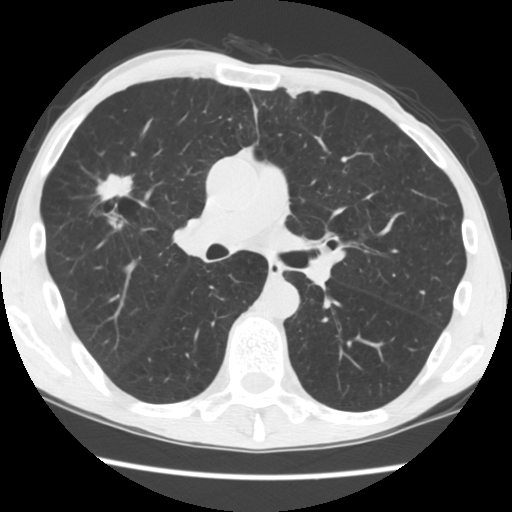
Axial slice from a low-dose chest CT screening exam; second annual screen; lung window (W 1500 / L -600 HU). Male participant, aged 56 years at enrolment. Current smoker at enrolment.
Lesion marked by an expert reader, box from (x=87, y=166) to (x=146, y=231) px. The screening reader recorded 2 non-calcified nodules or masses ≥4 mm on this exam (right upper lobe, left upper lobe); which of them this box marks is not recorded. Participant outcome: lung cancer diagnosed 101 days after this screen — squamous cell carcinoma, NOS, right upper lobe, right middle lobe, well differentiated (G1), stage IA (AJCC 6th edition), 27 mm at pathology.